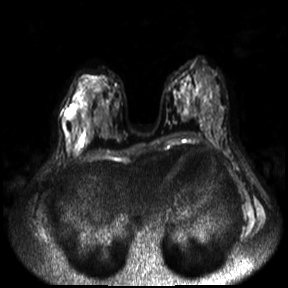
Breast MRI, one axial slice; diffusion-weighted series; image 2 of 4 stored at this slice position (different b-values; order by instance number); 3 T; 288 × 288 image matrix, field of view 360 × 360 mm. Female patient.
Annotated regions visible in this slice (outlined manually by an expert reader):
- tumour on diffusion-weighted imaging: bounding box [x1, y1, x2, y2] px = [65, 104, 76, 118]